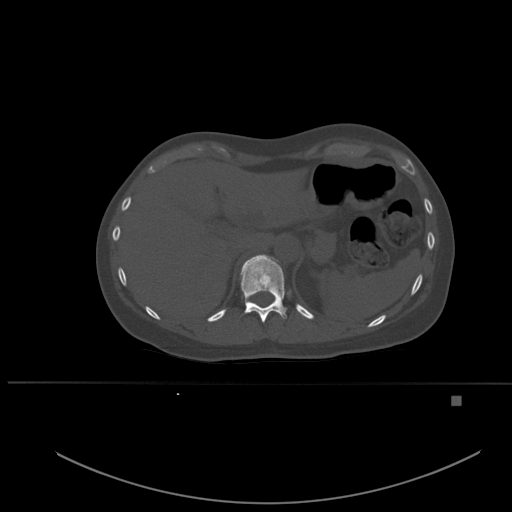
CT including the spine, one axial slice; position 271 of 651 along the scan axis; bone window (W 1800 / L 400 HU); 512 × 512 image matrix, field of view 443 × 443 mm. Female patient, age 49 years. From the clinical record (not read from this slice): primary cancer: breast; vertebrae with lytic lesions (as recorded): L3, T12, L4.
Outlined on this slice (semi-automatically segmented with operator editing):
- T11 vertebra: bounding box [x1, y1, x2, y2] px = [240, 255, 287, 323]